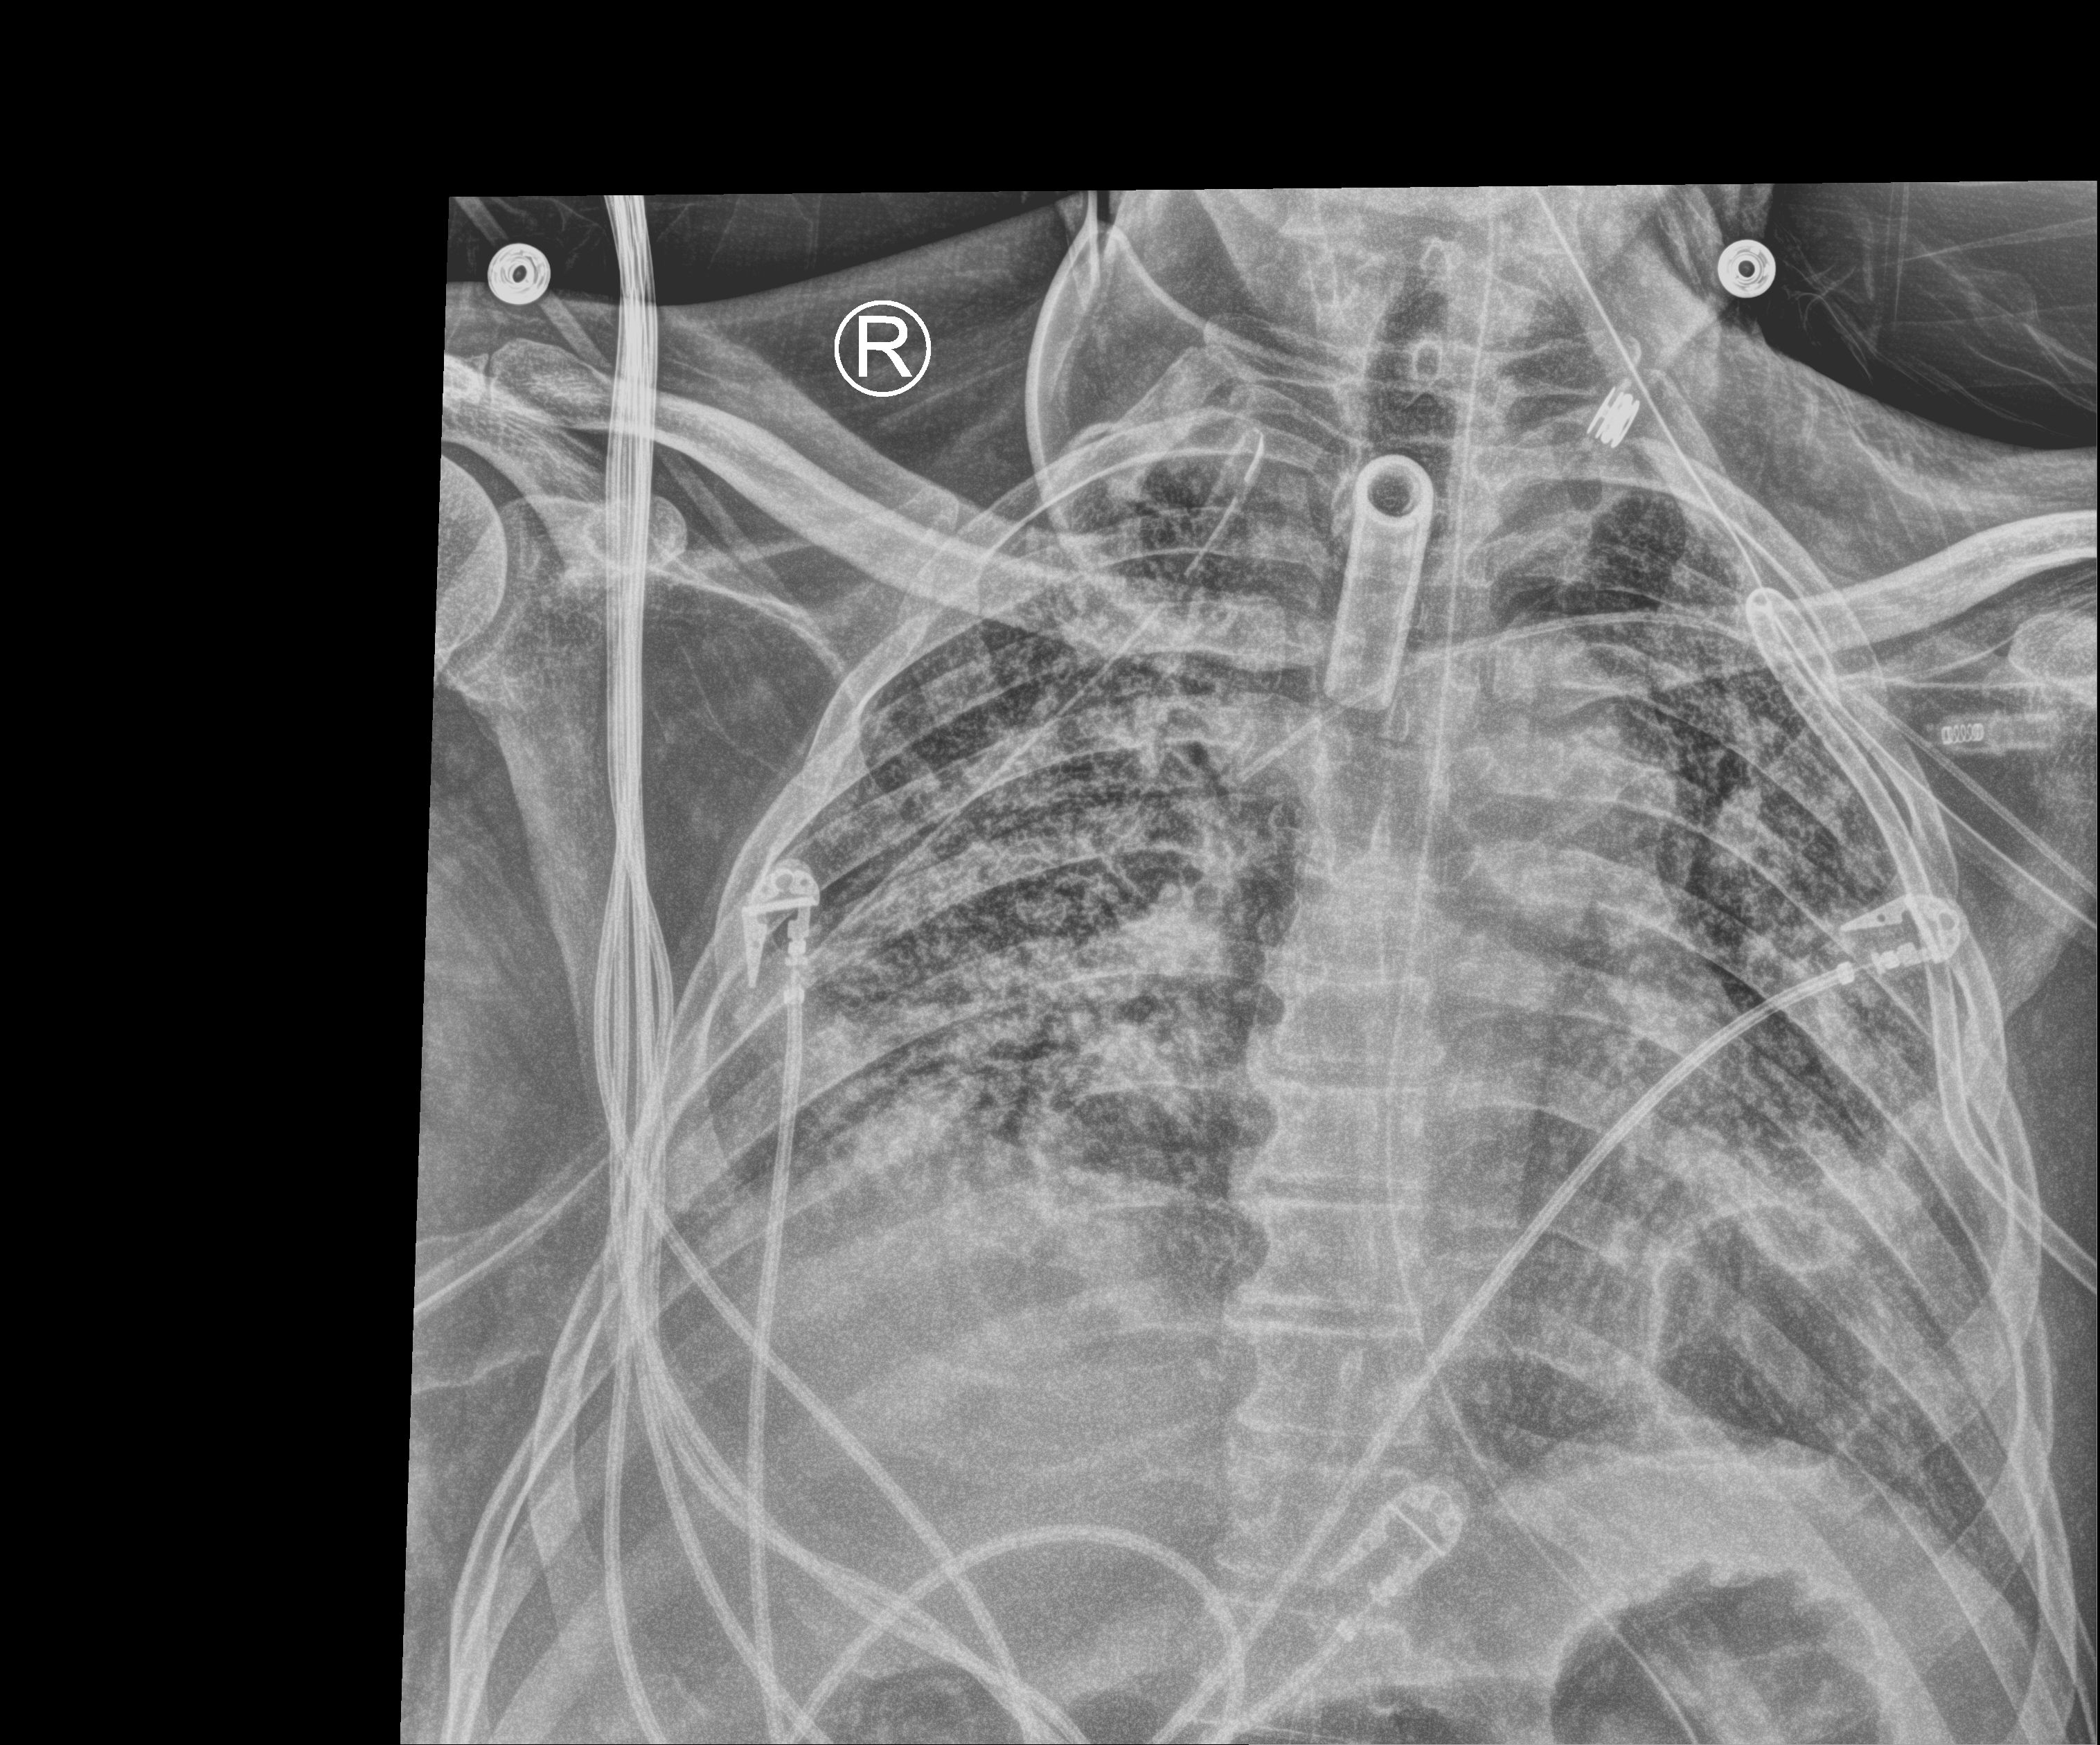
Portable chest radiograph; anteroposterior (AP) projection. Patient hospitalised with COVID-19; male, aged 18–59 years.
From the hospital-stay record, not from the radiograph (when in the stay this image was taken is not recorded): length of hospital stay: 83 days; mechanically ventilated during this hospital stay: yes.